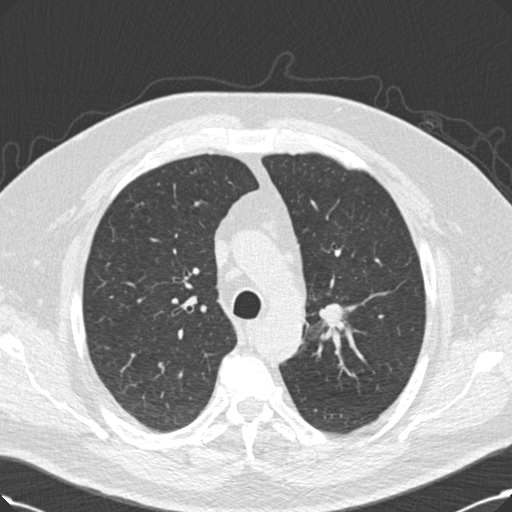
Chest CT (low-dose screening protocol), one axial image; third screening round (two years after baseline); lung window (W 1500 / L -600 HU); 120 kVp; 512 × 512 image matrix. Male, age 60 years at enrolment.
Expert-annotated lung lesion, bounding box [x1, y1, x2, y2] px = [318, 299, 349, 332]. The exam's reader record, not a measurement of the box and not confirmed to be the same lesion: non-calcified nodule or mass ≥4 mm, left upper lobe, 20 × 20 mm, smooth margins, soft tissue attenuation, pre-existing on the prior screen: no. Official screen result: positive, other. Later outcome: lung cancer diagnosed 53 days after this screen — squamous cell carcinoma, NOS, right upper lobe, 27 mm at pathology.